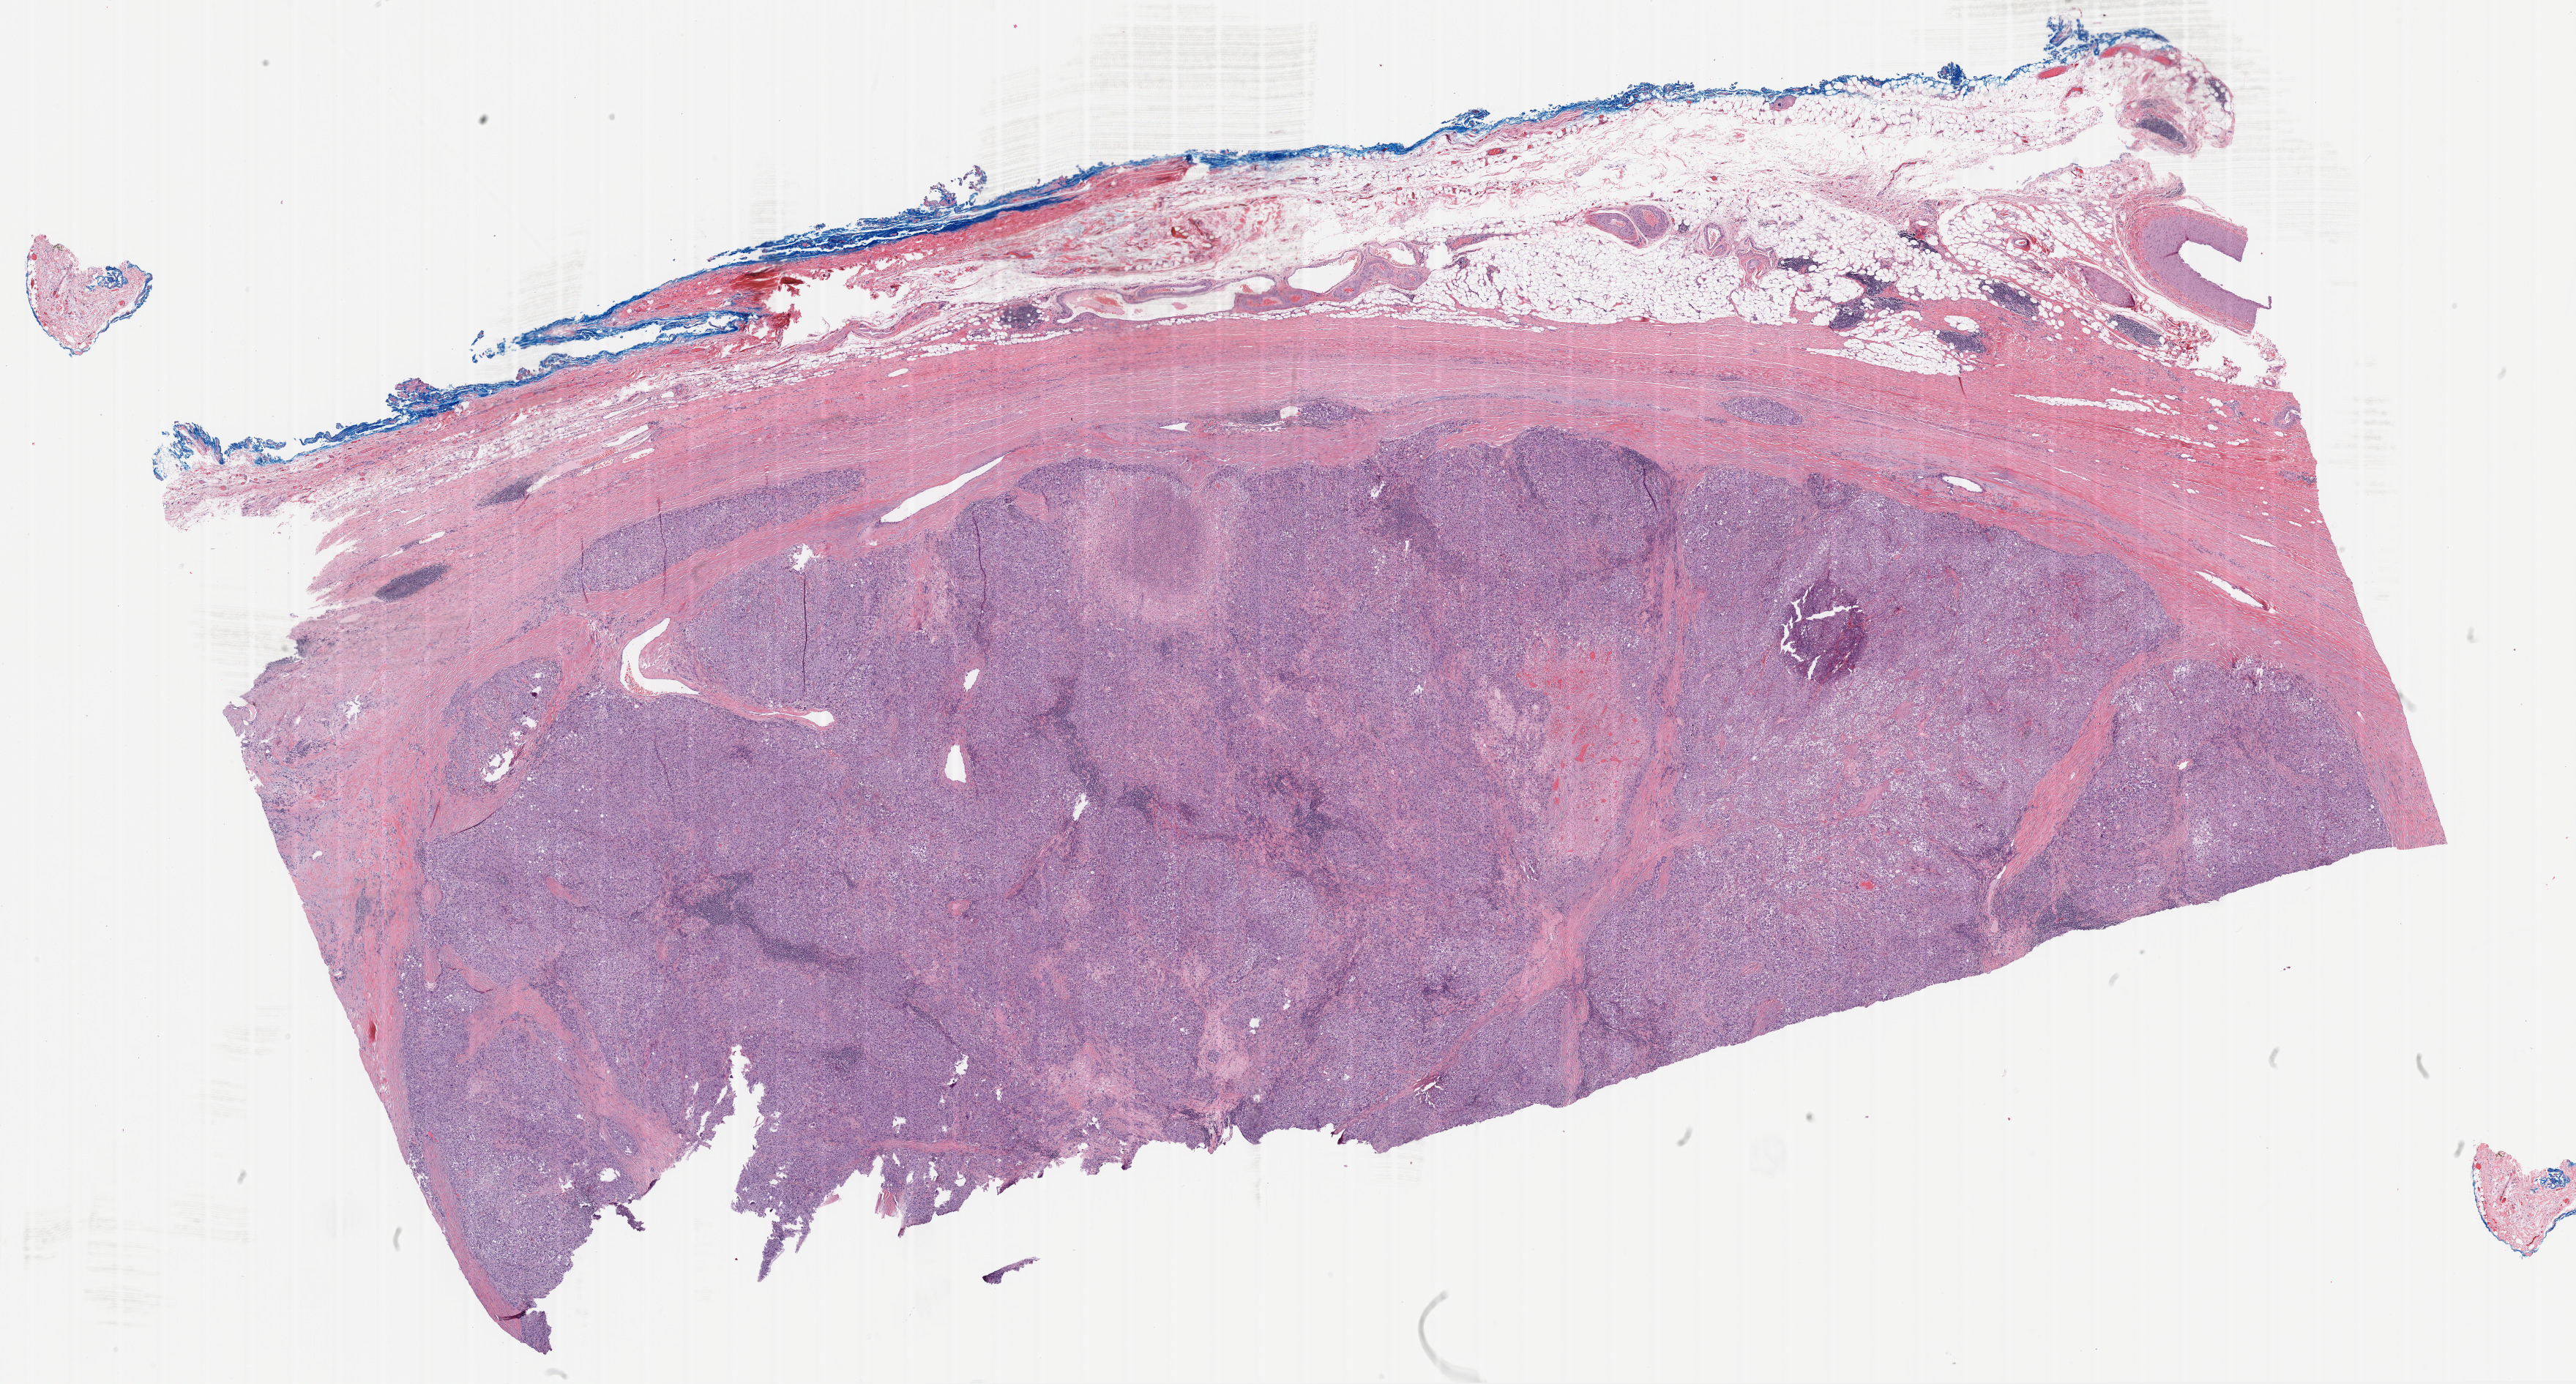
H&E-stained whole-slide image, low-resolution overview of the scanned area, about 28.4 x 15.3 mm (acquisition: 20x scan); formalin-fixed paraffin-embedded (FFPE) diagnostic section; metastatic tumour sample, sampled site: lymph nodes of axilla or arm. Female patient; age at initial diagnosis 59 years.
This section: metastatic tumour tissue. Patient diagnosis: Malignant melanoma, NOS.